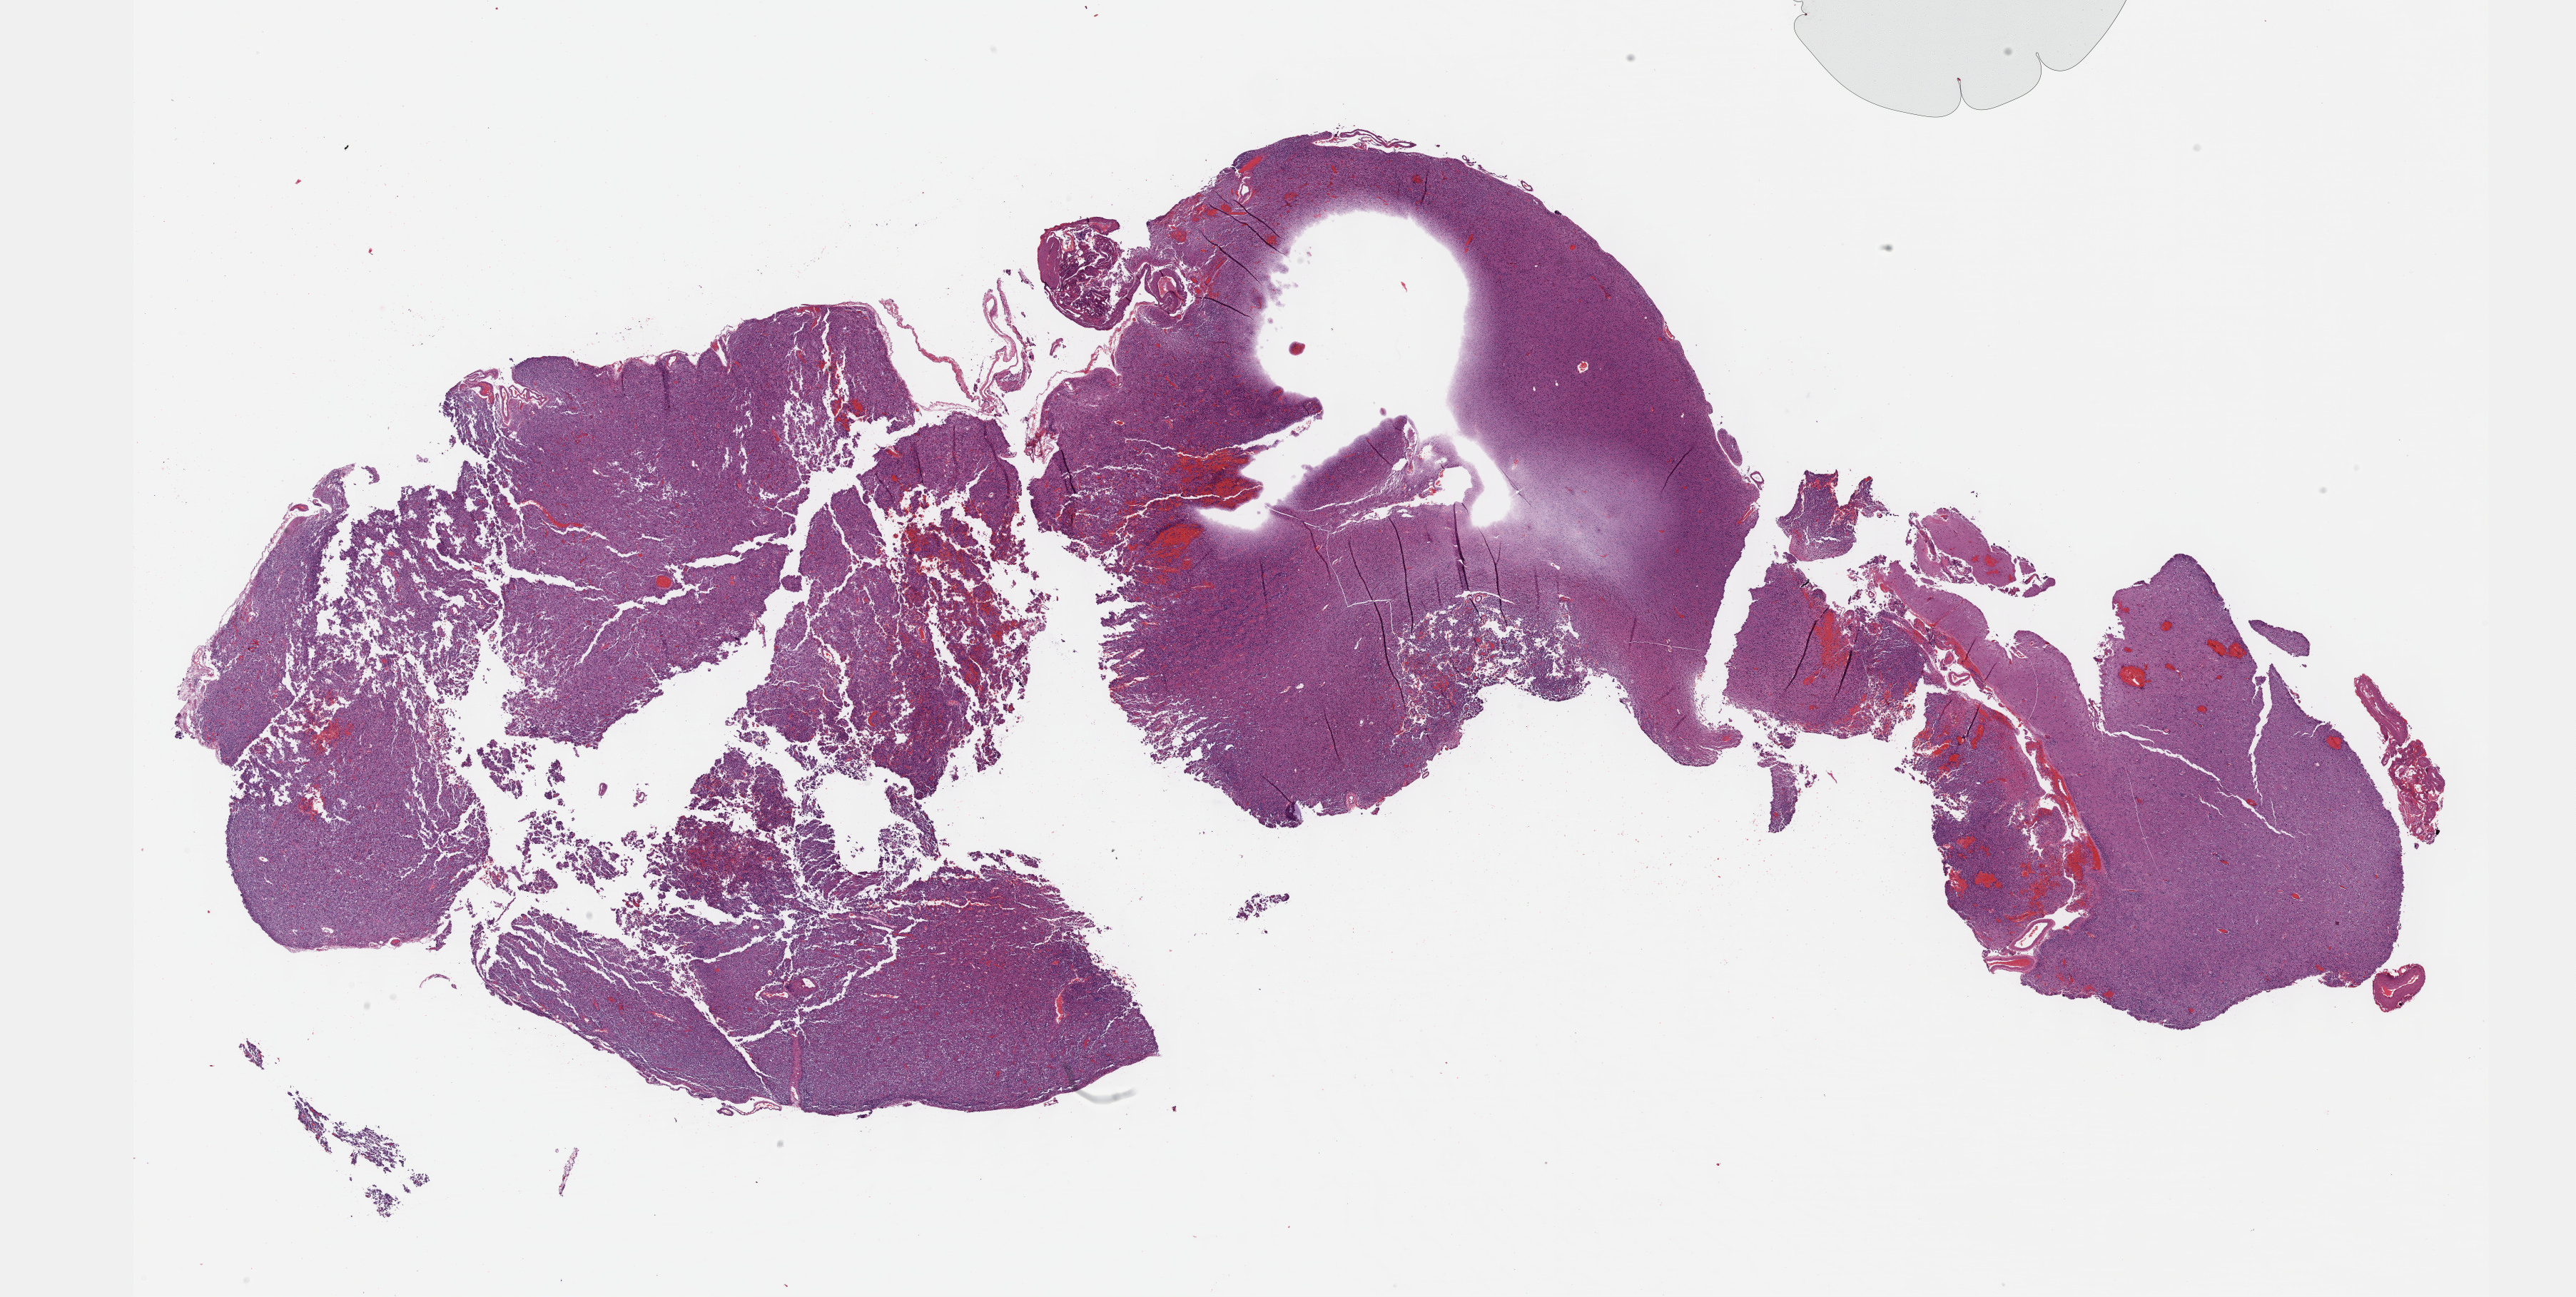
Hematoxylin and eosin (H&E) stained whole-slide image — a low-resolution overview of the entire scanned area, about 29.2 x 14.7 mm, formalin-fixed paraffin-embedded (FFPE) diagnostic section, sample: primary tumour, brain. Male, age 59 years at initial diagnosis. Histologic grade: G3 (poorly differentiated).
Histologic diagnosis: Oligodendroglioma, anaplastic.